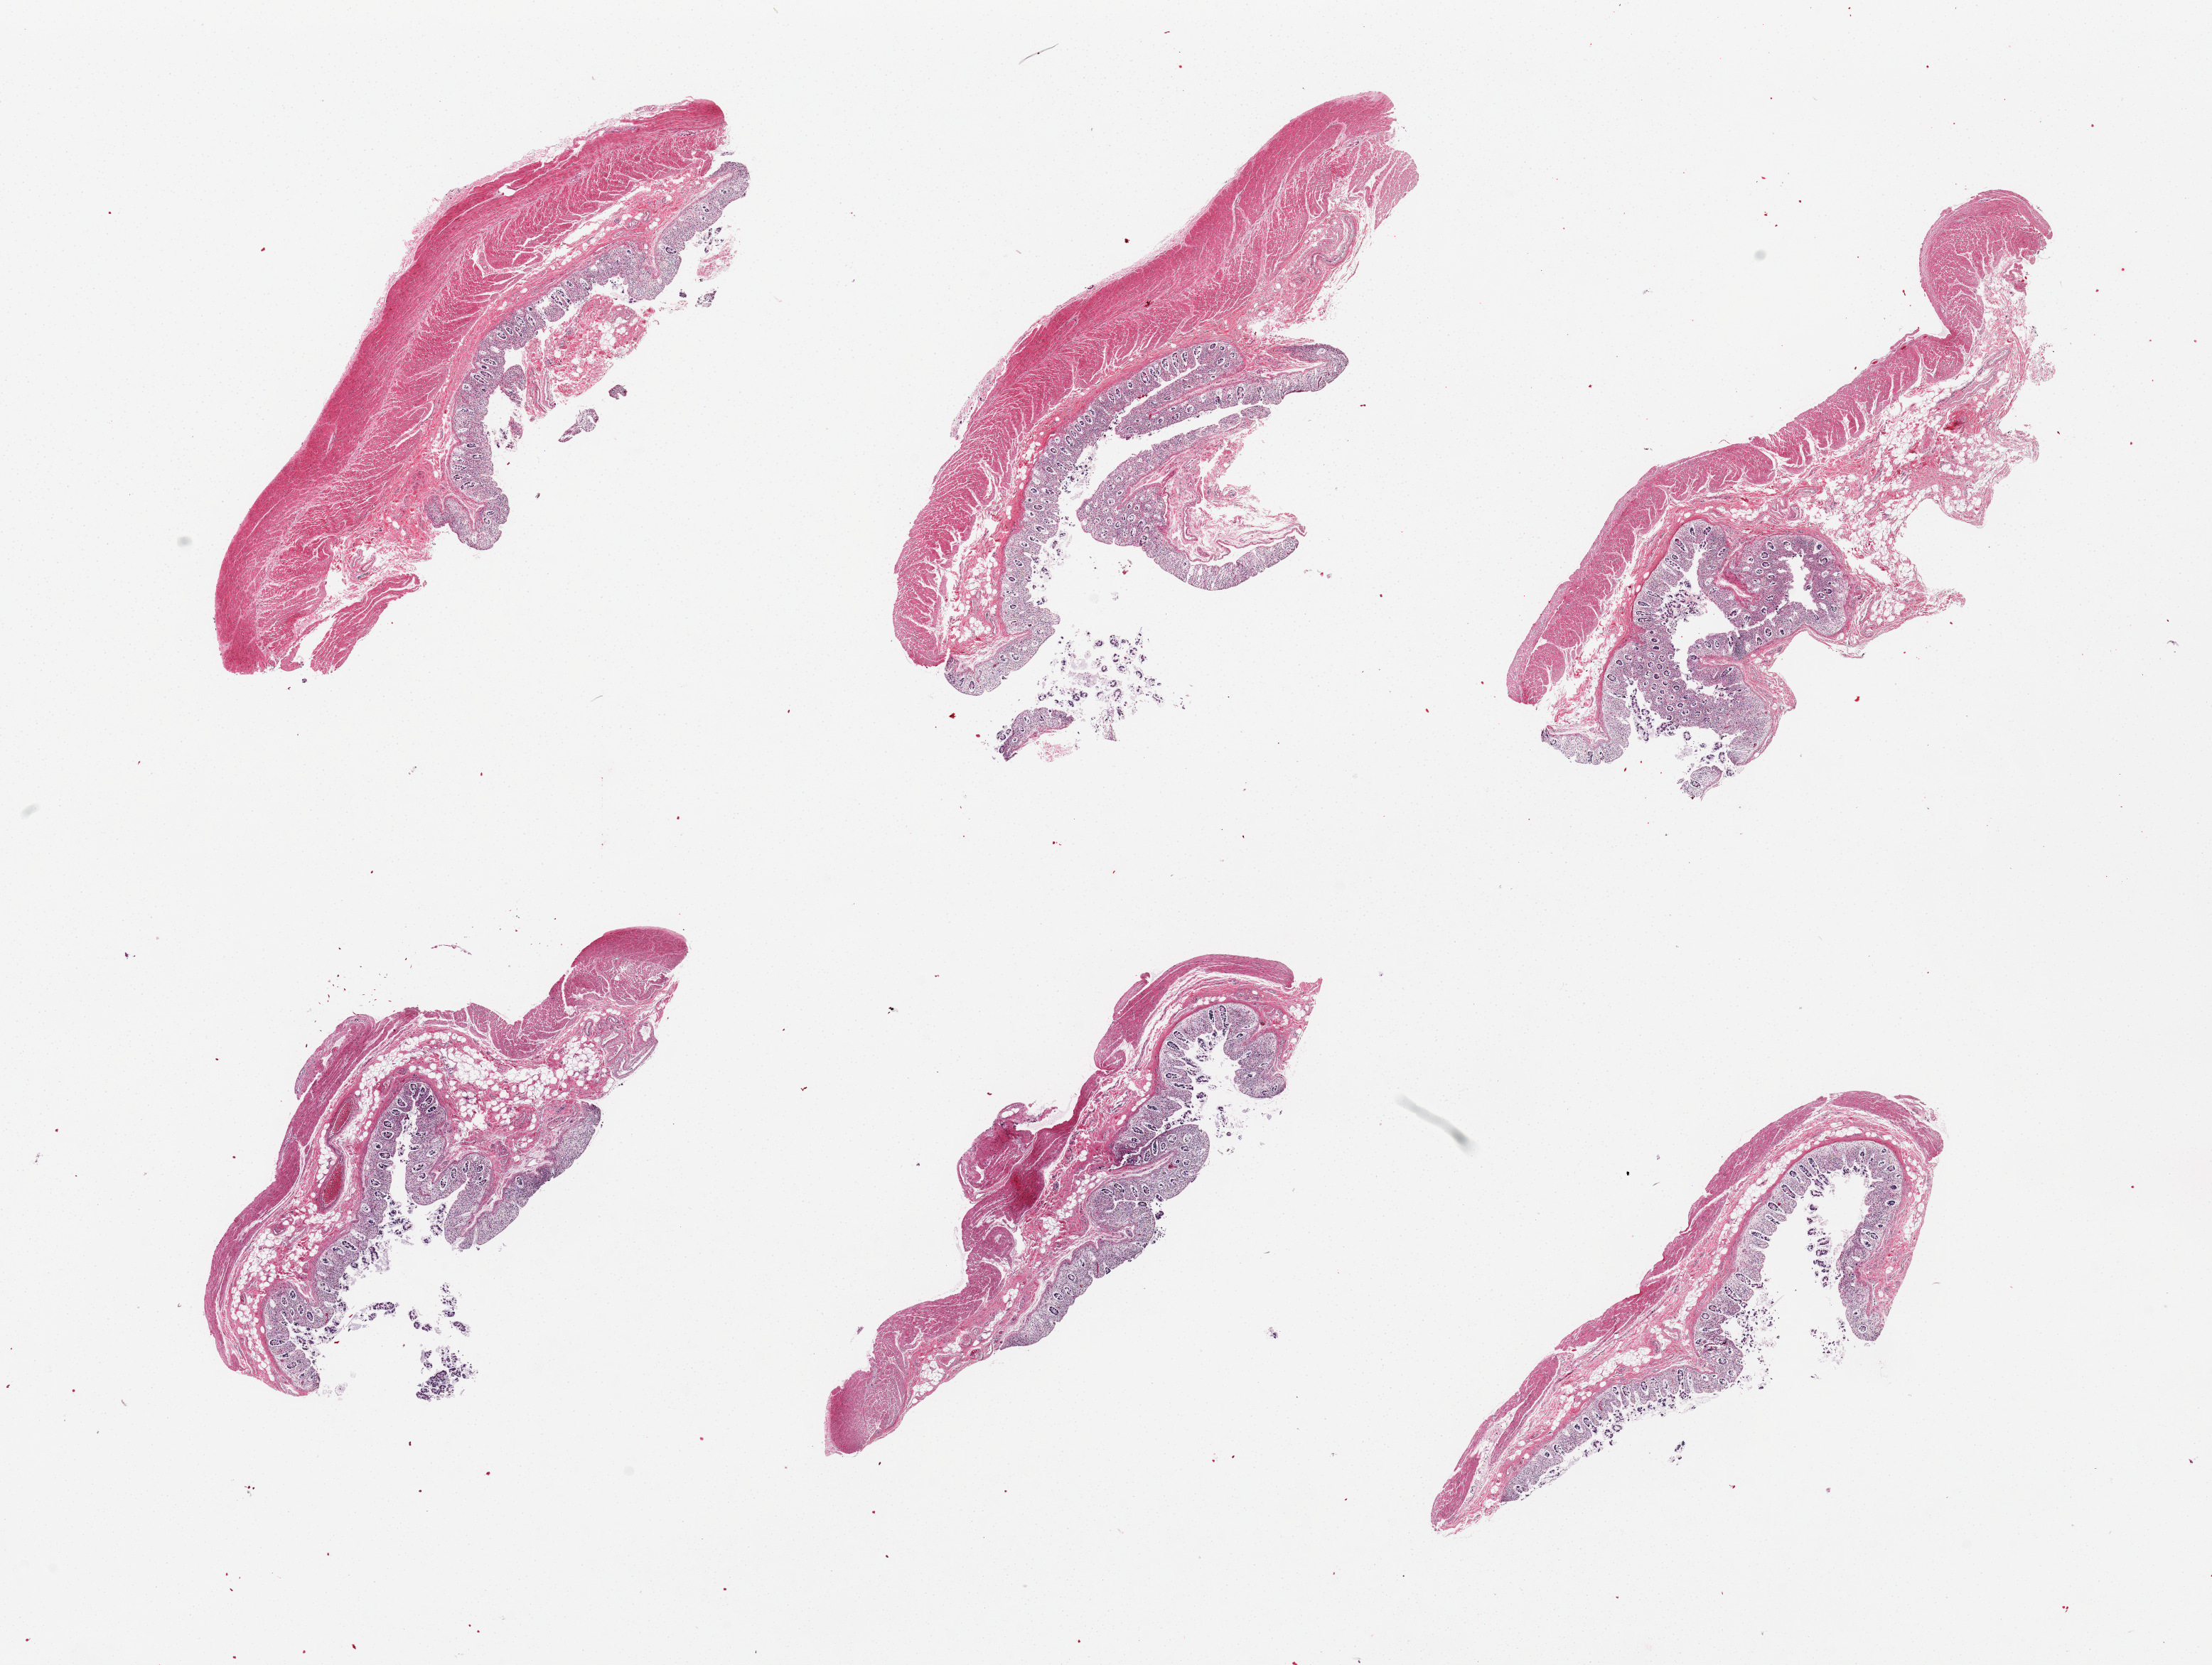
Hematoxylin and eosin (H&E) whole-slide image, brightfield, low-resolution overview of the scanned area, about 24.6 x 18.5 mm (slide scanned at 20x). PAXgene-fixed, paraffin-embedded tissue. Target tissue: transverse colon. Donor tissue sample. Donor sex: female.
Pathologist's review note for this sample: 6 pieces, mucosa badly autolyzed, ~10% thickness.